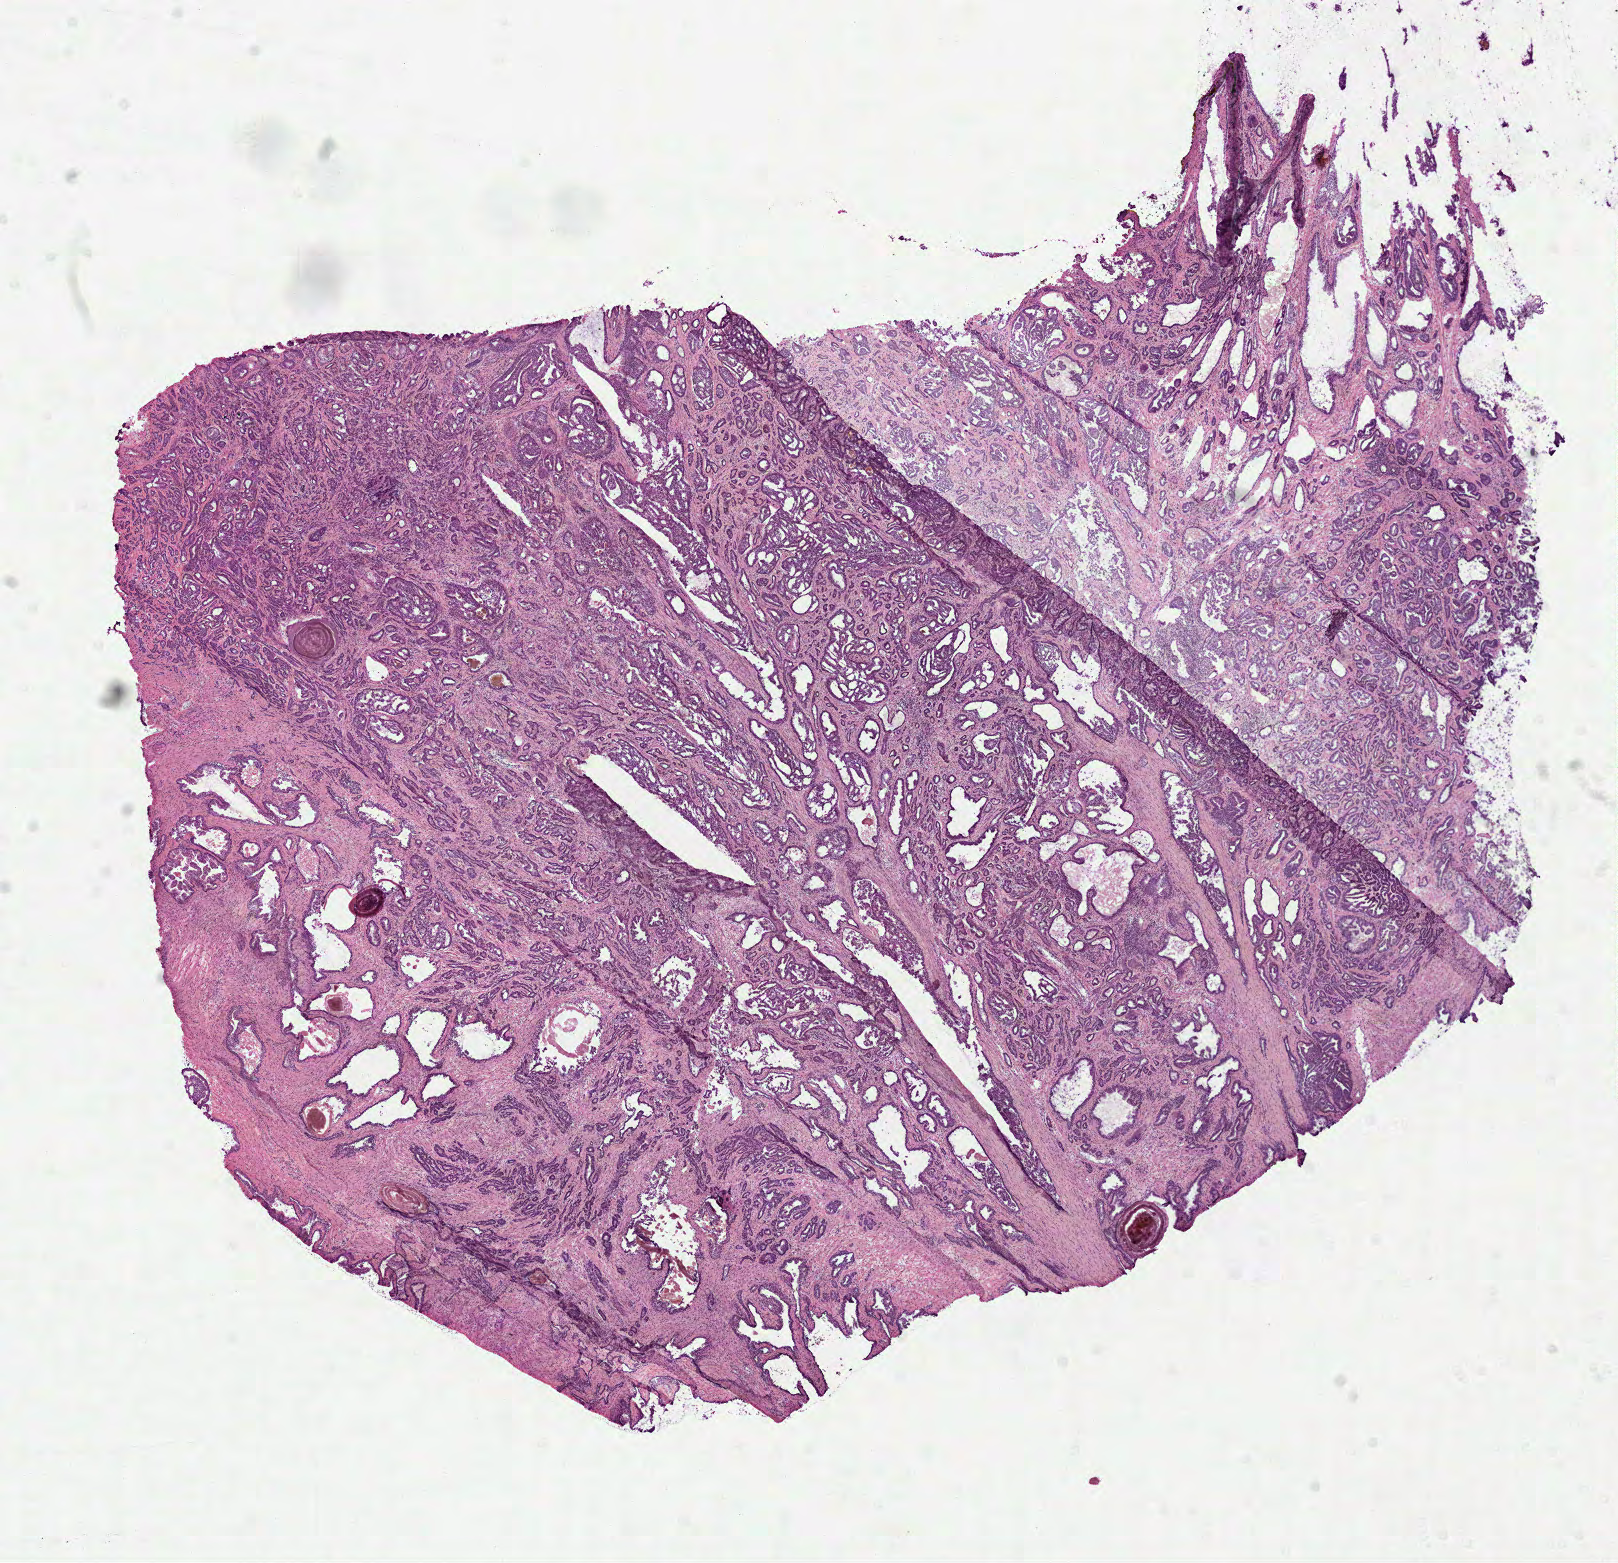
Digitized Hematoxylin and eosin (H&E) stained tissue section (whole slide), a low-resolution overview of the entire scanned area, about 13.1 x 12.6 mm; frozen section; prostate, primary tumour sample. Male patient; age at initial diagnosis 67 years. Gleason score: 7 (3+4). Pathologist review of this section (percent, as recorded): tumour cells 75%, tumour nuclei 78%, normal cells 10%, stromal cells 15%, necrosis 1%. Infiltration values recorded for this section: lymphocyte infiltration 1%, monocyte infiltration 0%, neutrophil infiltration 0%.
Pathologic diagnosis: Acinar cell carcinoma (prostate gland).